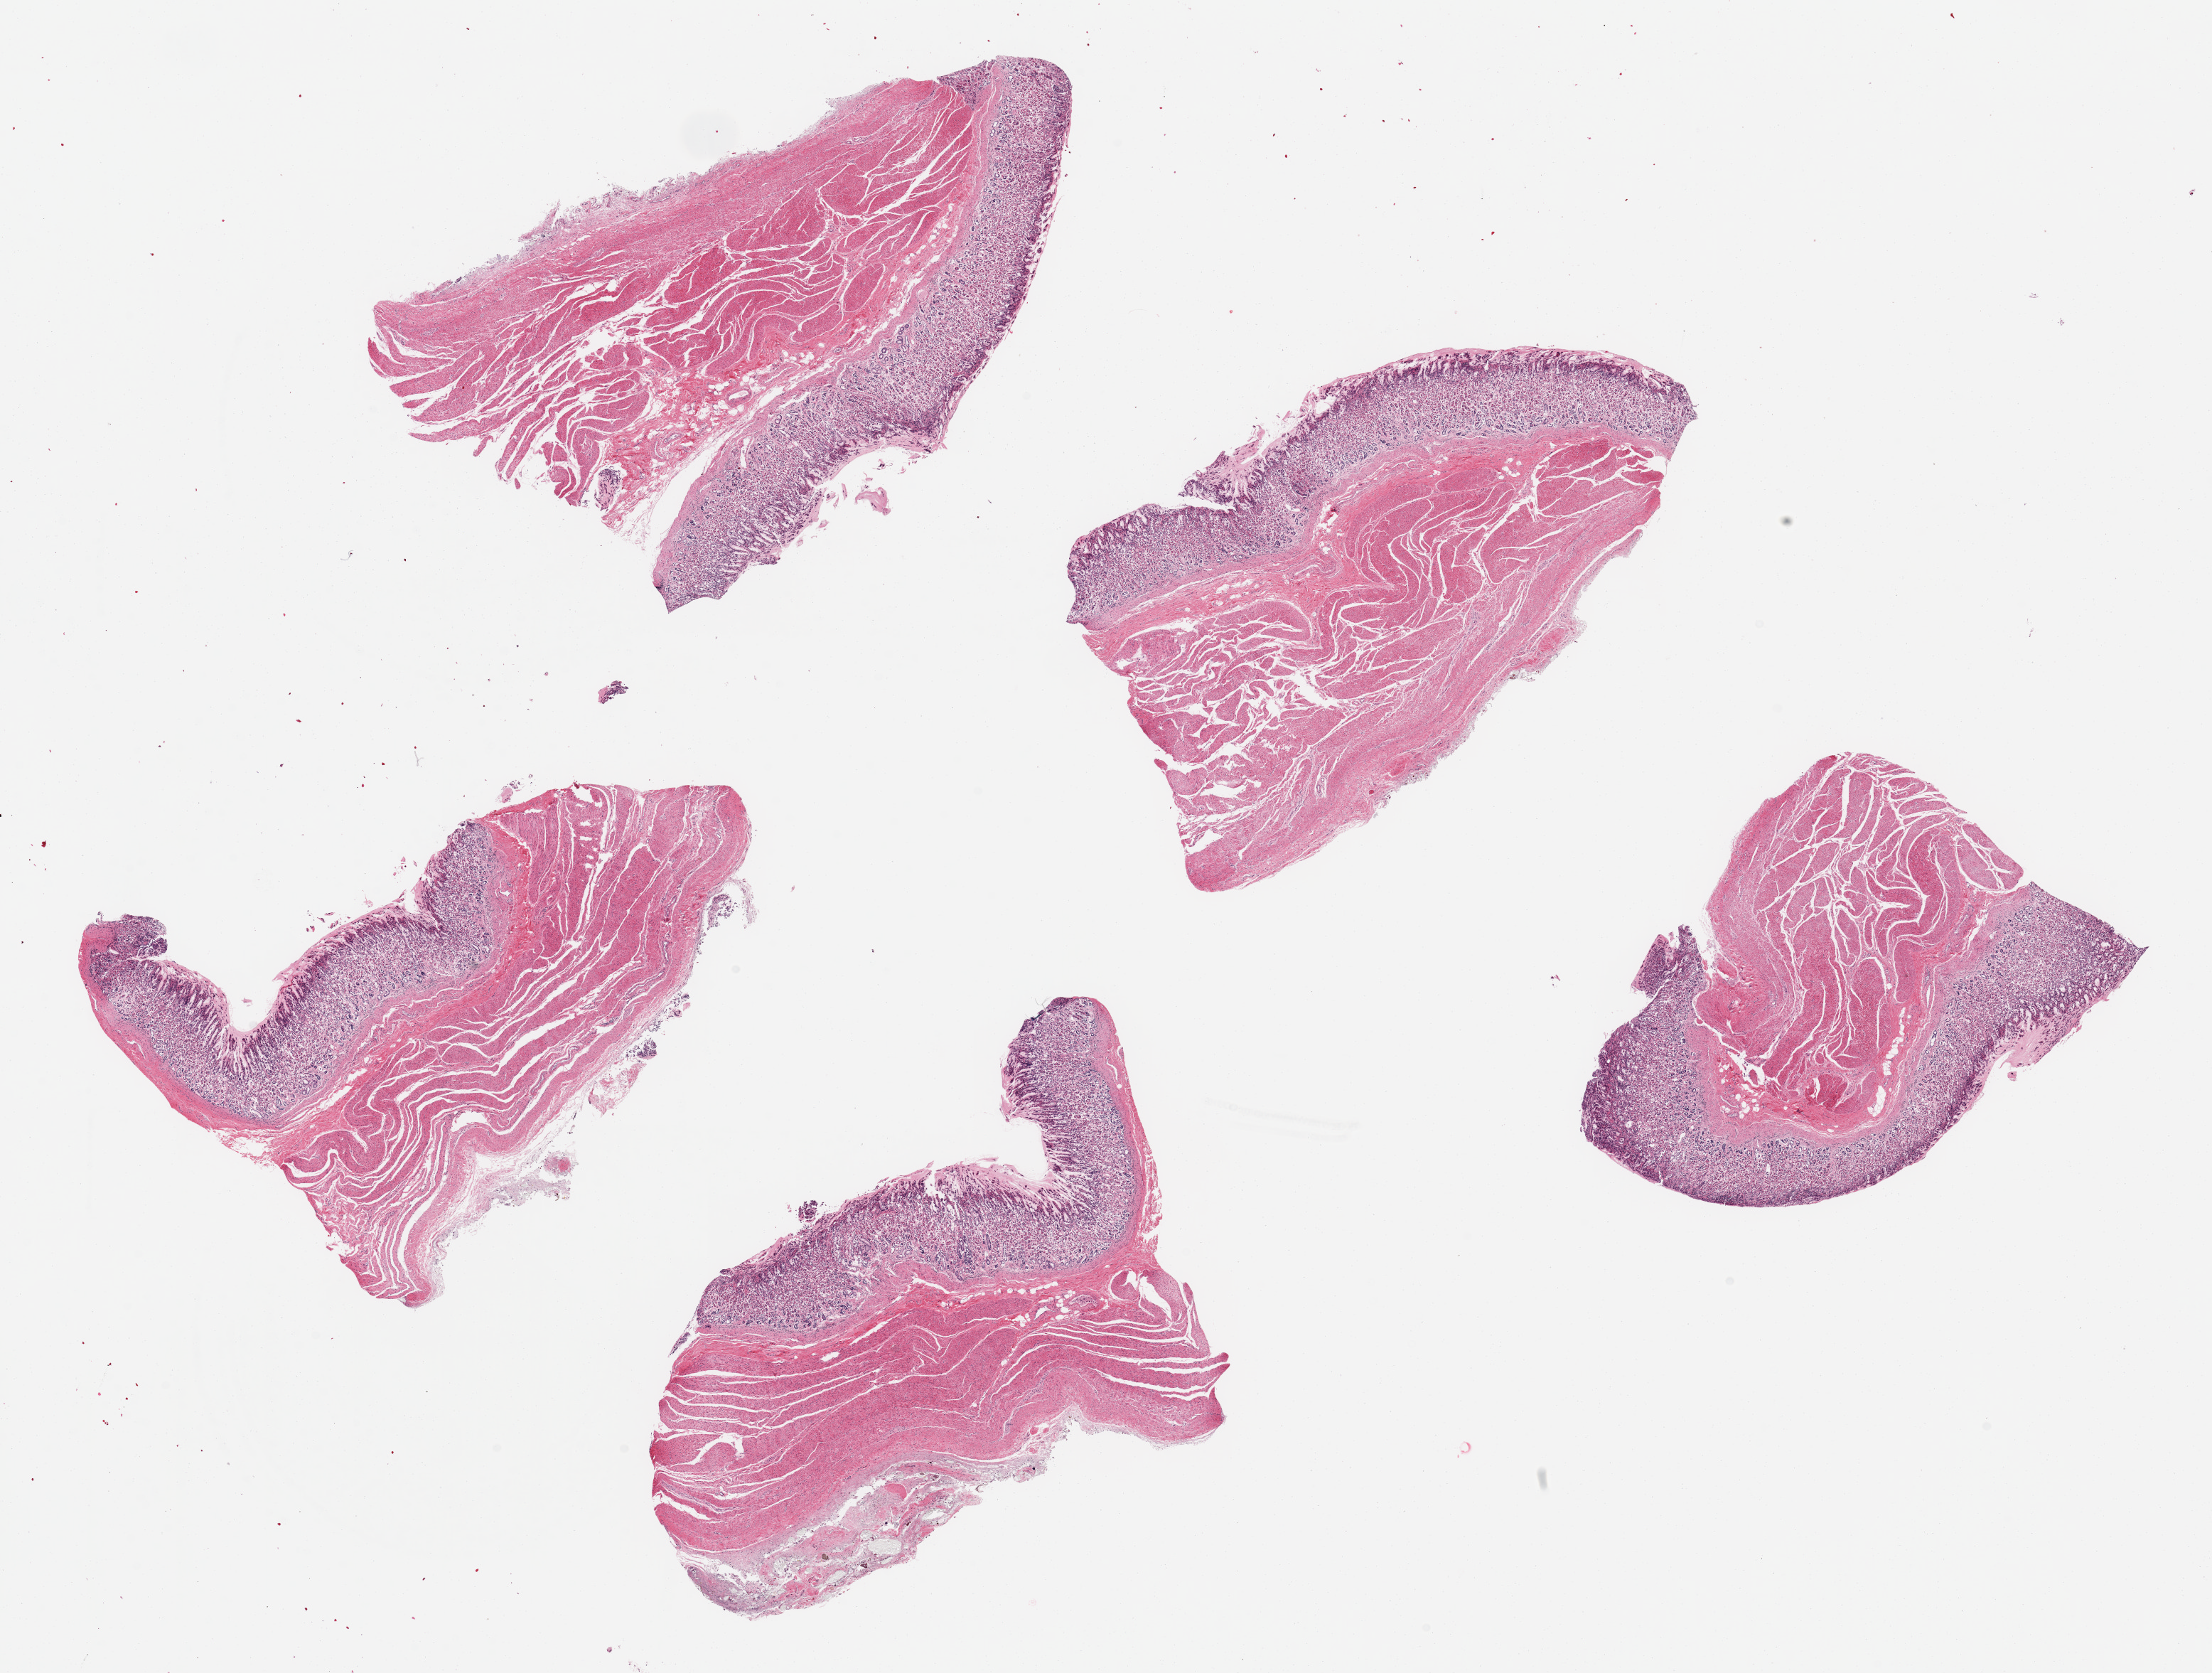
Hematoxylin and eosin (H&E) whole-slide image, shown as a low-resolution overview of the whole scanned area (about 24.6 x 18.6 mm); PAXgene-fixed, paraffin-embedded tissue; sampled site (target tissue): stomach; tissue donor sample. Donor: male.
* reviewer comment on this tissue sample: 6 pieces, ~6x3.5mm, mucosa is 25-30% of thickness